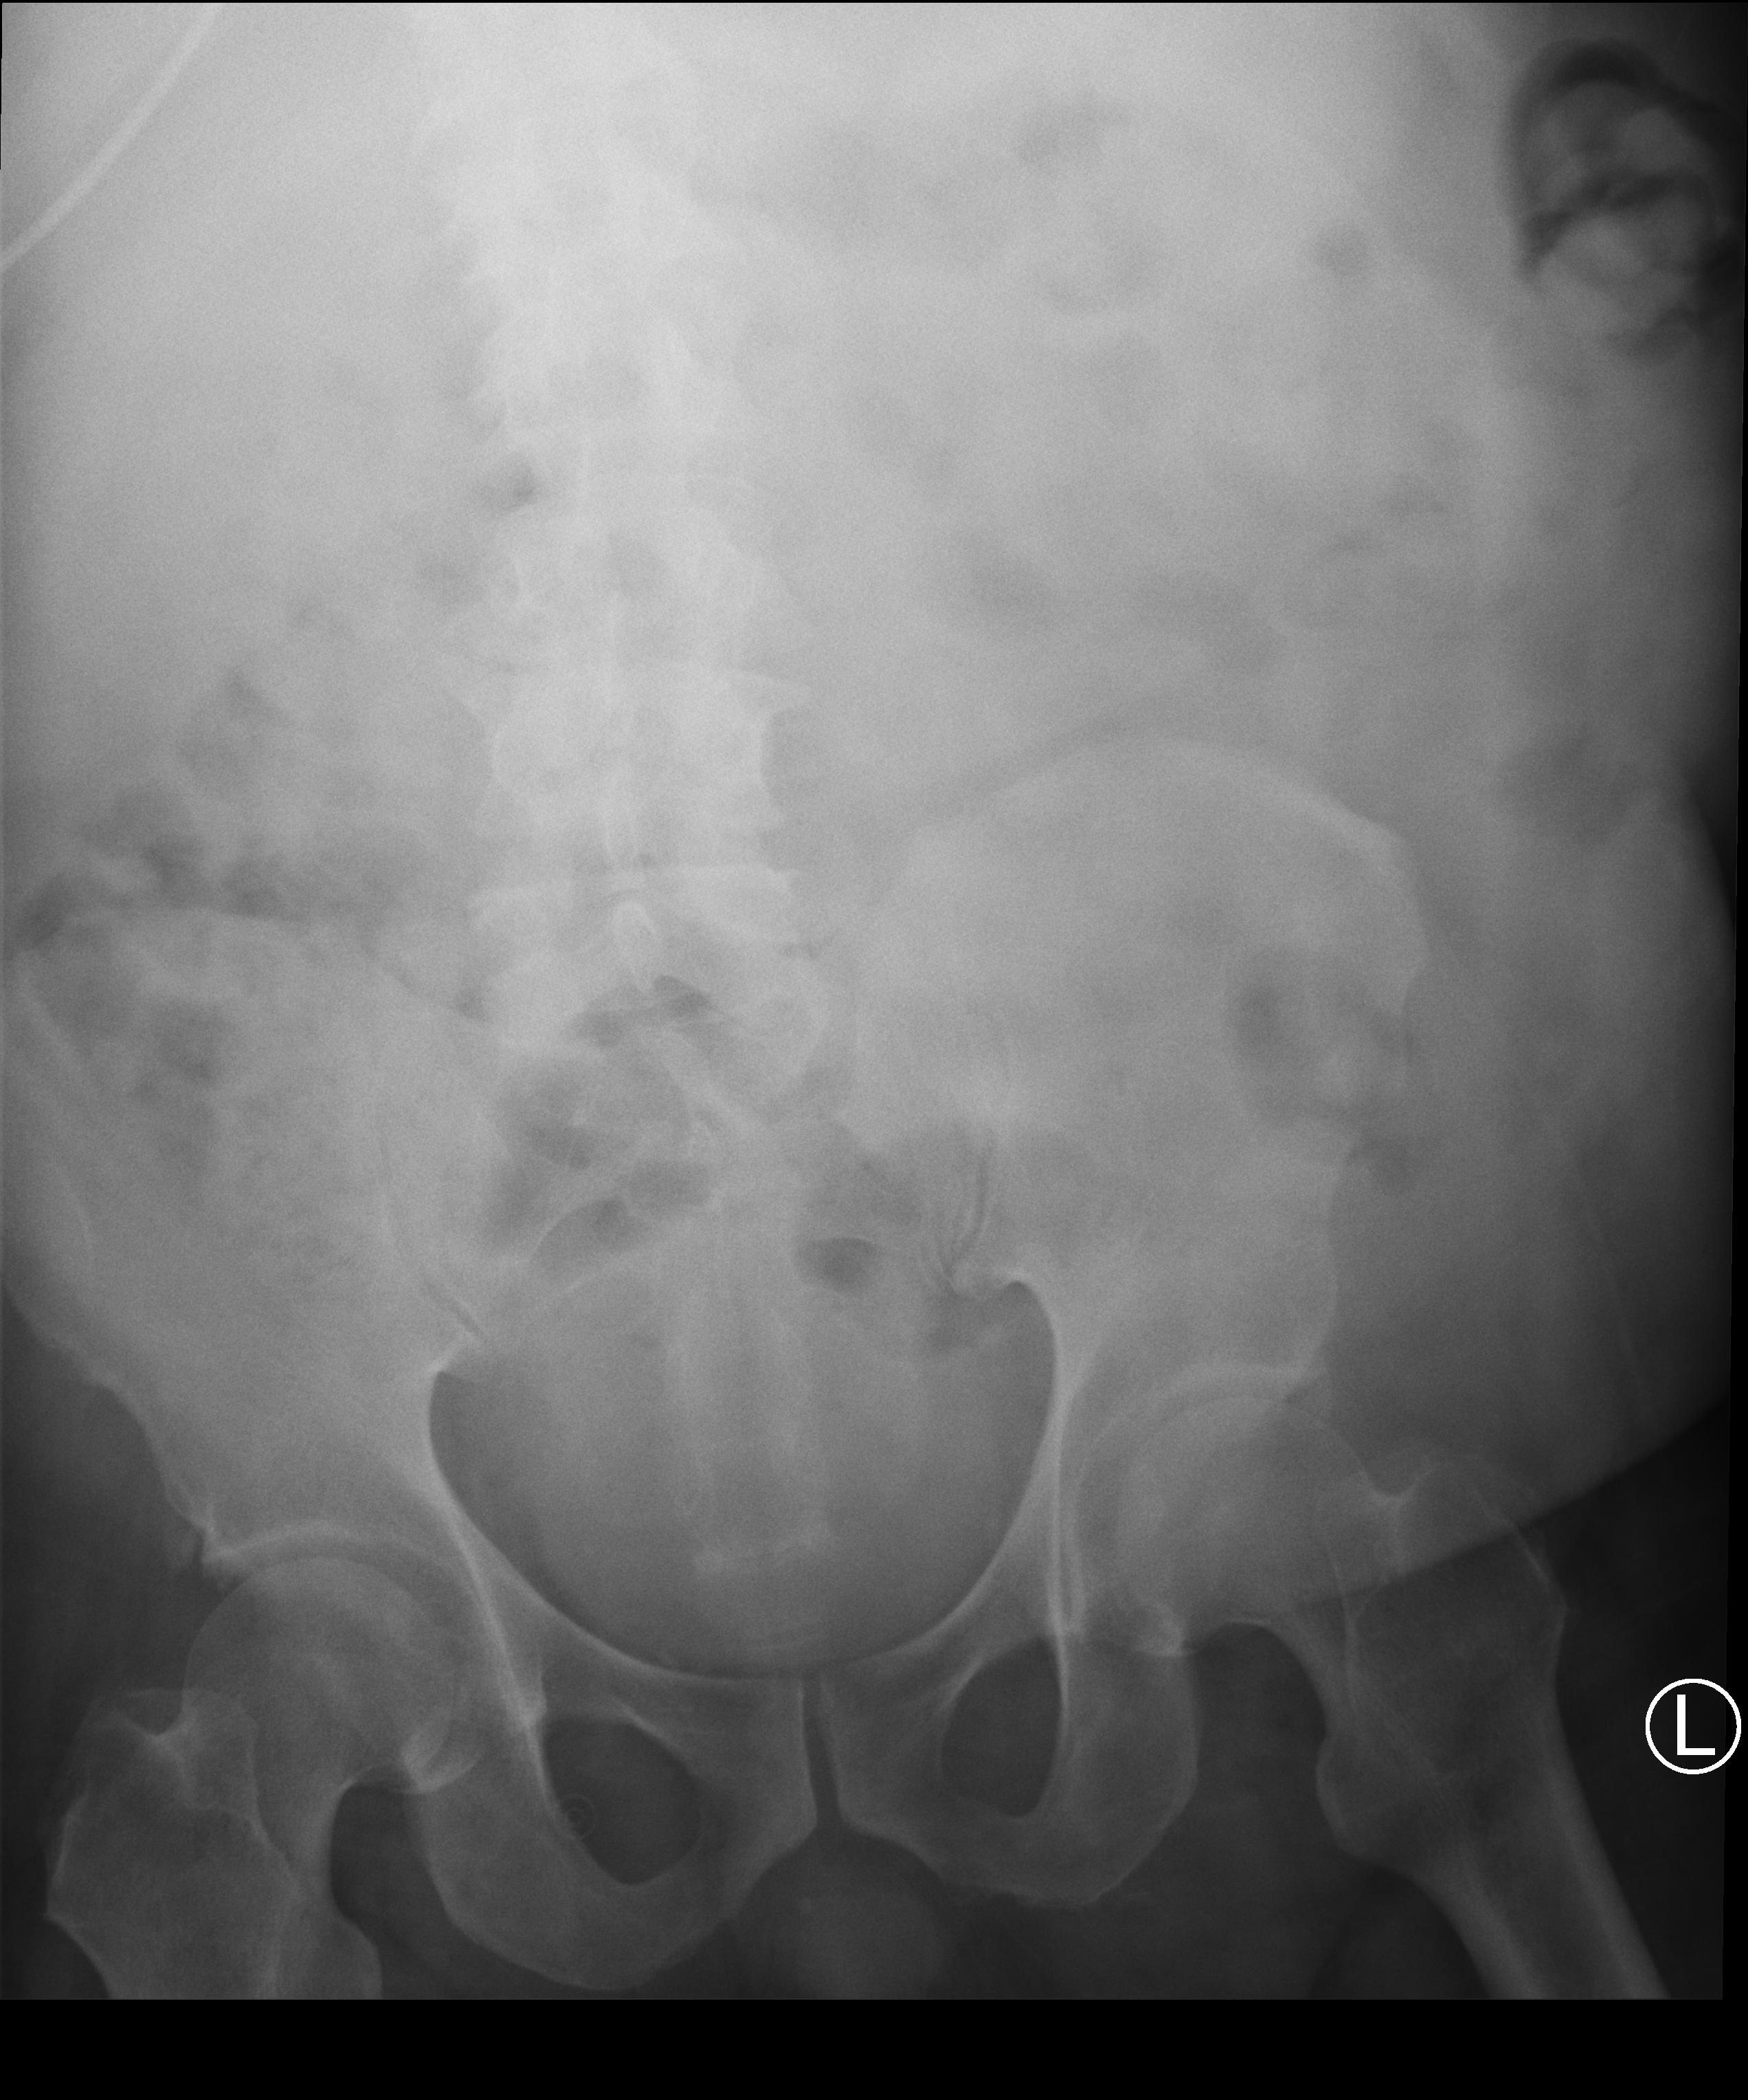
Abdomen X-ray (portable), anteroposterior (AP) projection. Male patient hospitalised with COVID-19, age 18–59 years.
Hospital-stay facts (about this admission, not read from this image; timing relative to this image not recorded):
- admitted to intensive care during this hospital stay: no
- chronic kidney disease (admission record): no